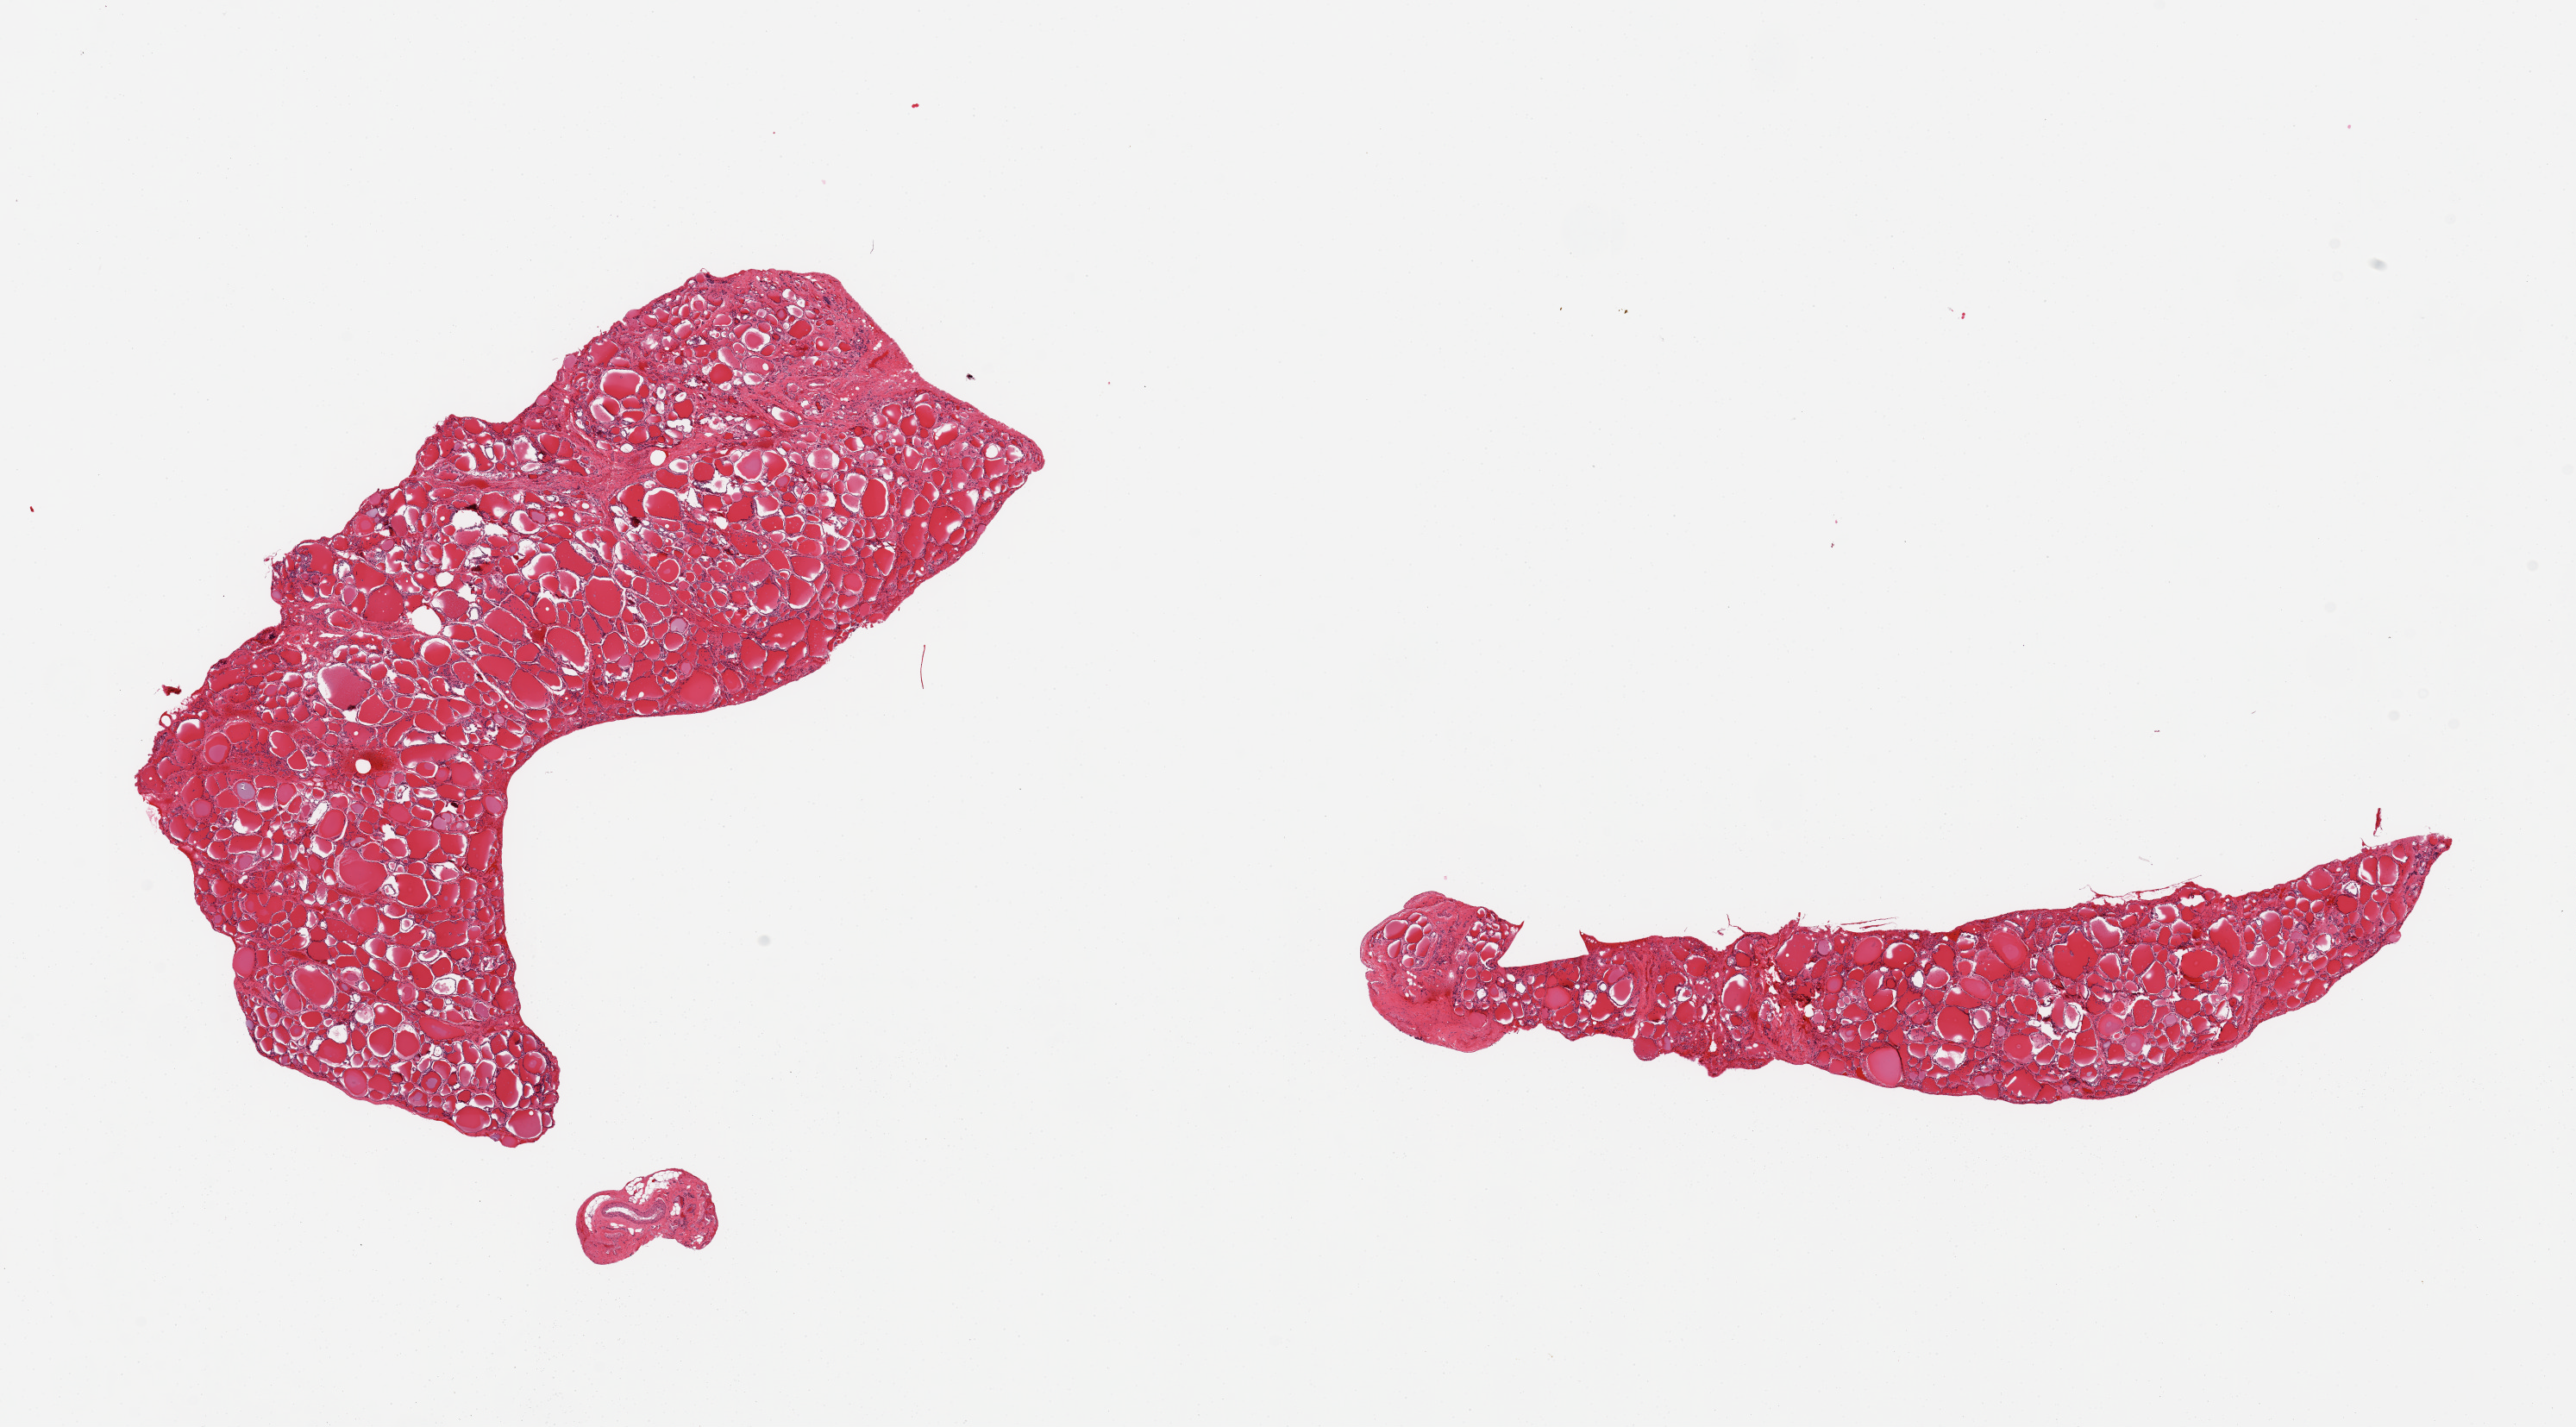
Whole-slide image, haematoxylin and eosin stain — shown as a low-resolution overview of the whole scanned area (about 23.6 x 13.1 mm), PAXgene-fixed, paraffin-embedded tissue, sampled site (target tissue): thyroid, donor tissue sample.
* pathologist's review note for this sample: 2 pieces